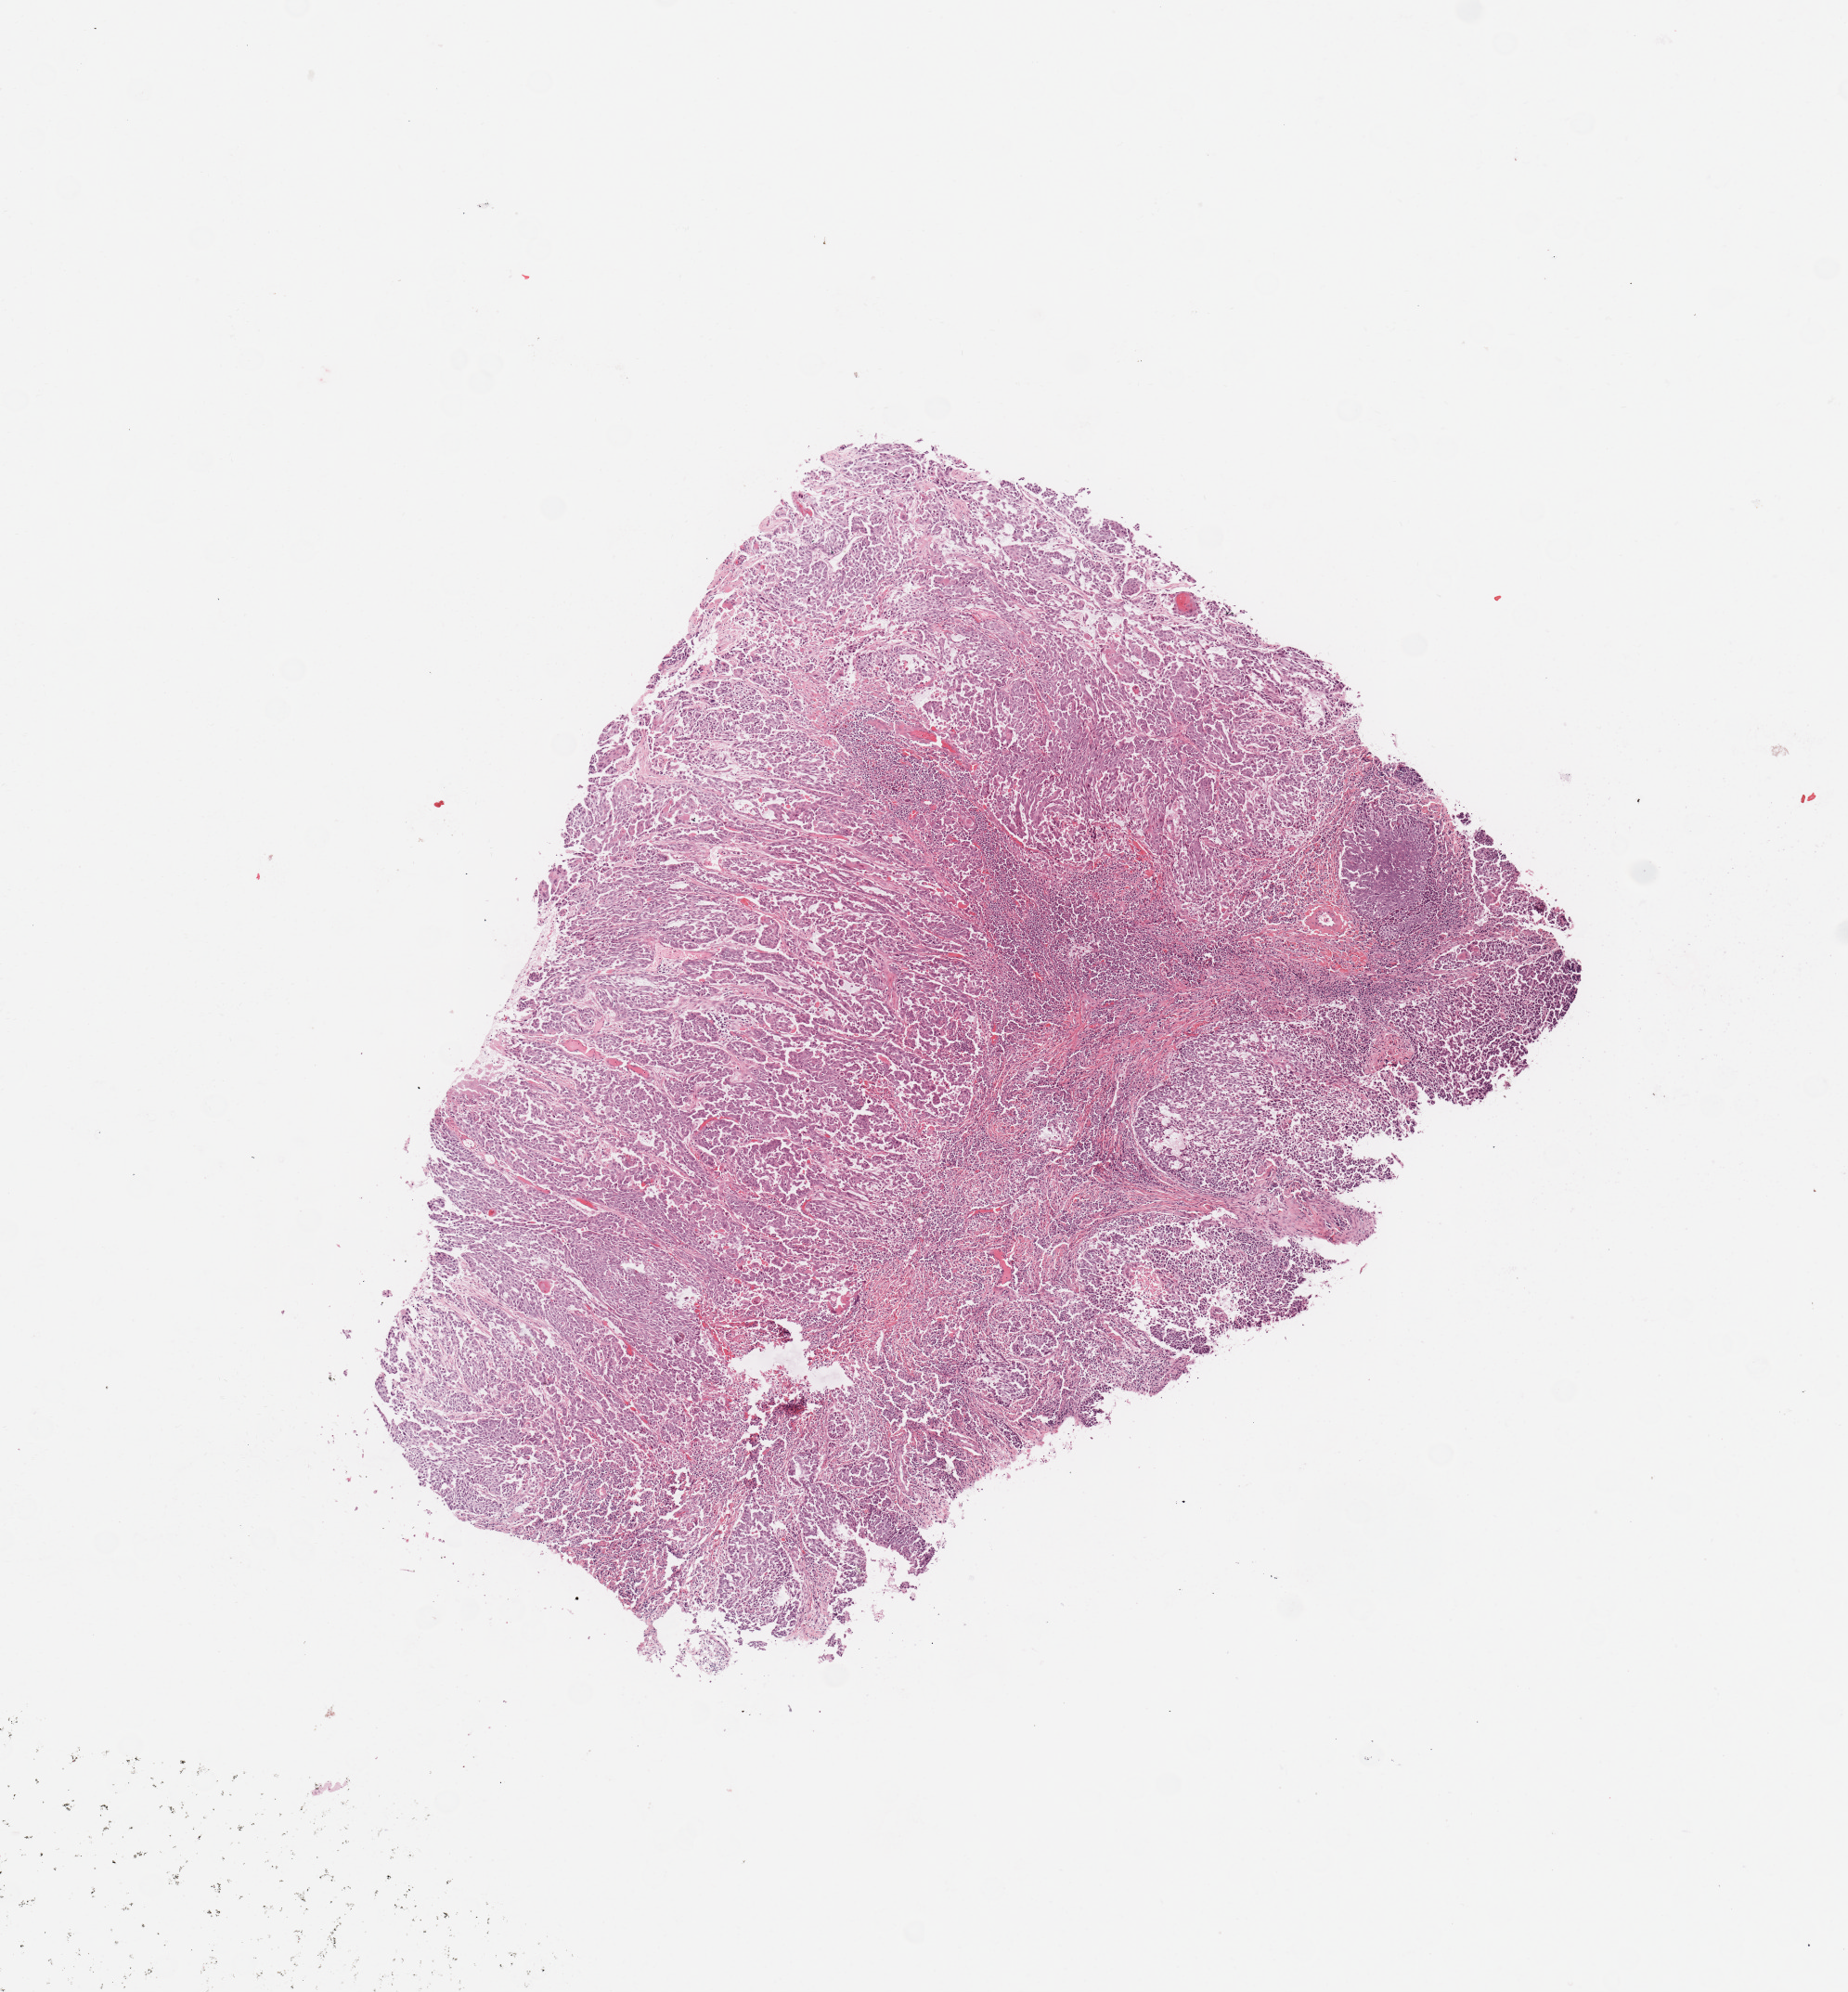
Digitized Hematoxylin and eosin (H&E) stained tissue section (whole slide), shown as a low-resolution overview of the whole scanned area (about 7.9 x 8.5 mm); tumour tissue sample, sampled site: supraglottis. Patient: male, age 59 years. Histologic grade: G3 (poorly differentiated). Pathologist review of this section (percent, as recorded): tumour nuclei 90%, necrosis 5%.
- histologic diagnosis: Squamous cell carcinoma, NOS
- AJCC pathologic stage: III
- primary tumour site (as recorded): larynx